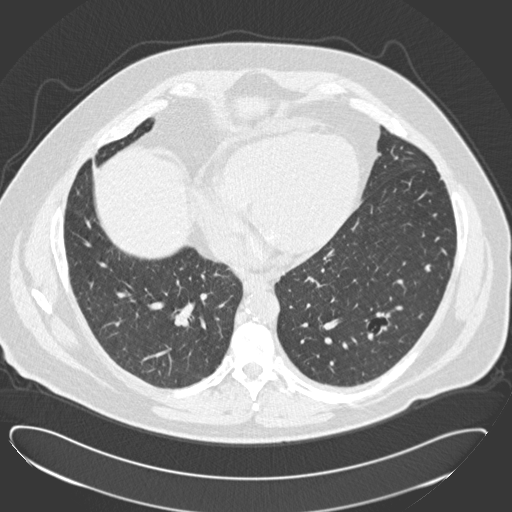
Low-dose screening chest CT, axial slice; baseline annual screen; lung window (W 1500 / L -600 HU); slice 93 of 183 in the series; 512 × 512 image matrix. Male participant, aged 57 years at enrolment. Current smoker at enrolment.
Expert reader's lesion annotation, box from (x=356, y=301) to (x=409, y=353) px. The screening reader recorded 2 non-calcified nodules or masses ≥4 mm on this exam (left lower lobe, left lower lobe); which of them this box marks is not recorded. Official screen result: positive, change unspecified: nodule(s) >= 4 mm or enlarging nodule(s), mass(es), or other non-specific abnormalities suspicious for lung cancer. Lung cancer was diagnosed 791 days after this screen (after the third annual screen): squamous cell carcinoma, NOS, left lower lobe, moderately differentiated (G2), stage IA (AJCC 6th edition), 22 mm at pathology.